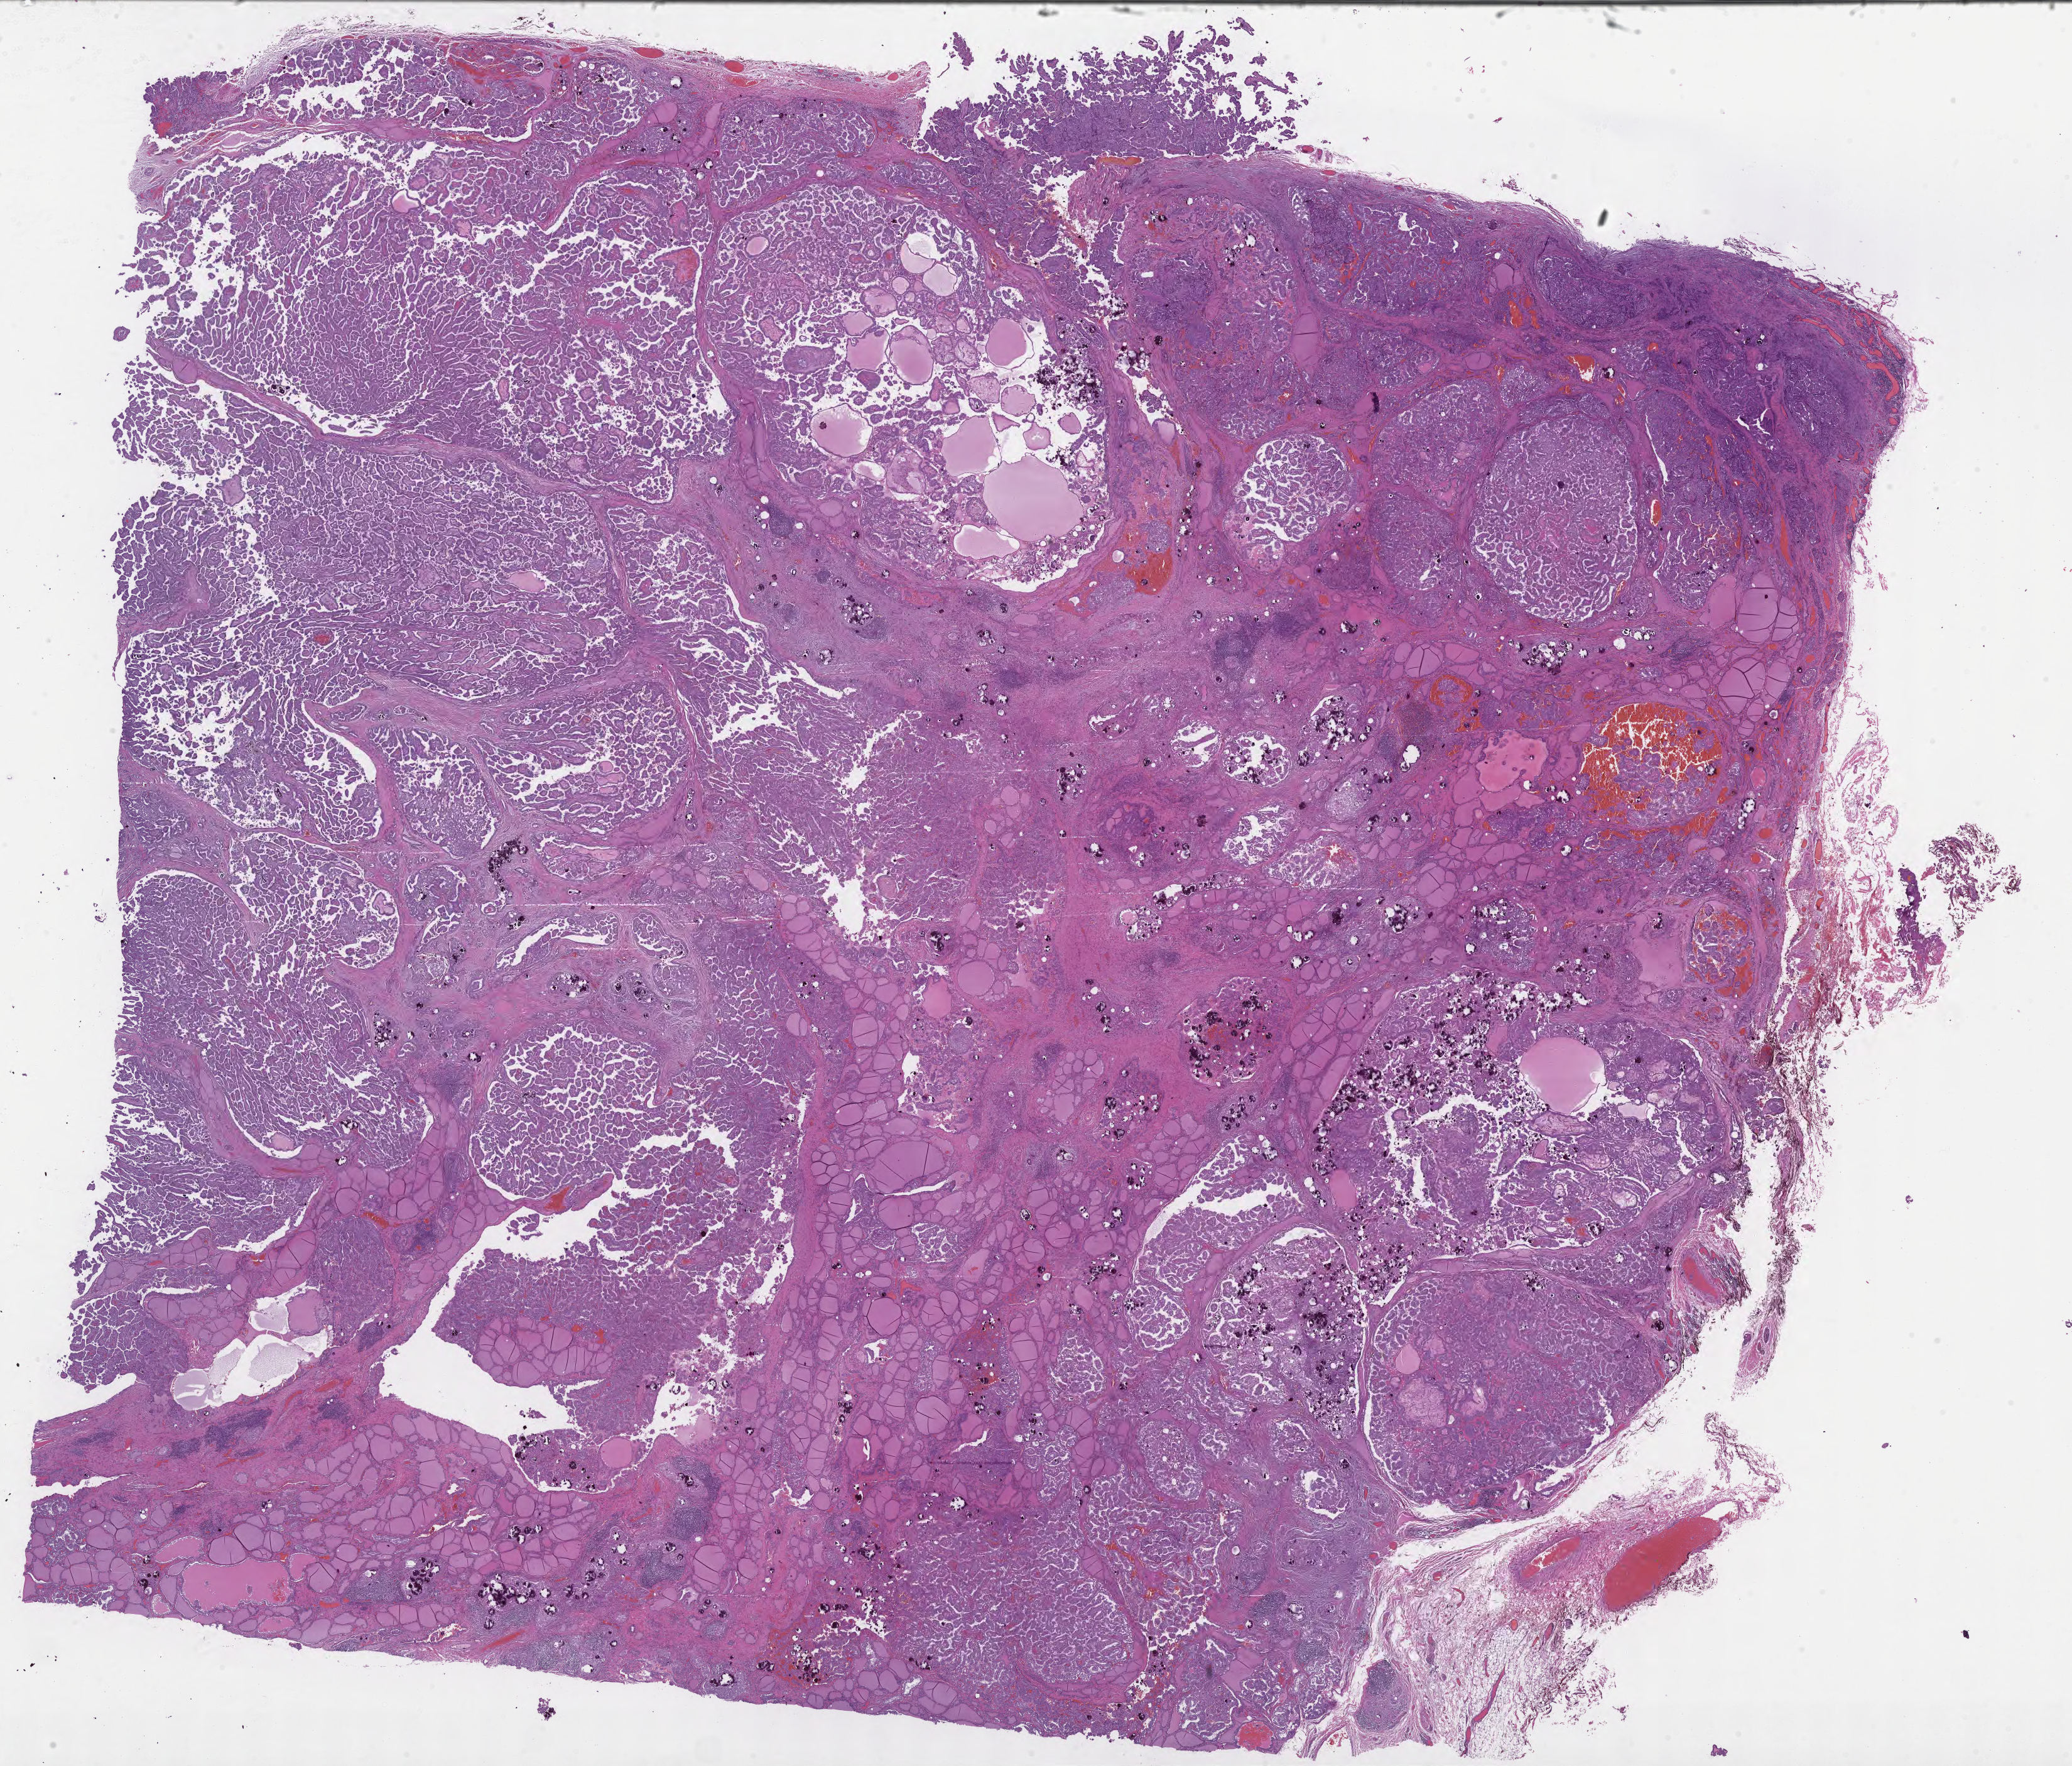
Hematoxylin and eosin (H&E) whole-slide image of tumor tissue from the thyroid, shown as a low-resolution overview of the whole scanned area (about 26.7 x 22.7 mm). Formalin-fixed paraffin-embedded section. Patient male; age 210 months (17 years 6 months).
• diagnosis (ICD-O-3 morphology term): Papillary carcinoma, NOS